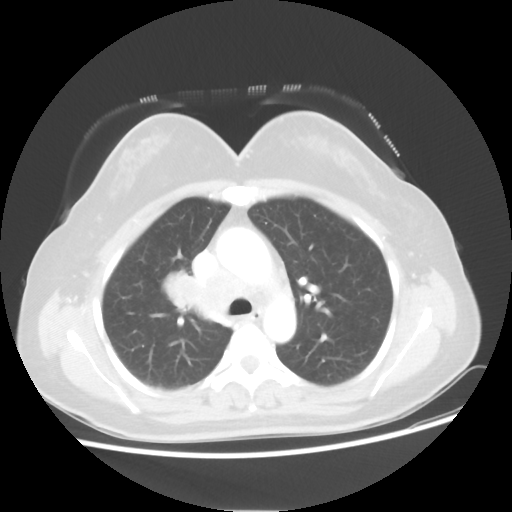
Chest CT, one axial slice. Position 34 of 50 along the scan axis. 100 kVp. Lung window (W 1500 / L -600 HU). 5 mm slice thickness. 512 × 512 image matrix, field of view 360 × 360 mm. Female patient, age 40 years. From the clinical record (not read from this slice): clinical TNM (as recorded): T1c N3 M0; histopathological grade: G3.
Structures marked on this image (rectangle marked by the reading radiologist):
- lung tumour (recorded histology: small cell carcinoma): bounding box (x1, y1, x2, y2) in pixels: (167, 268, 202, 319)